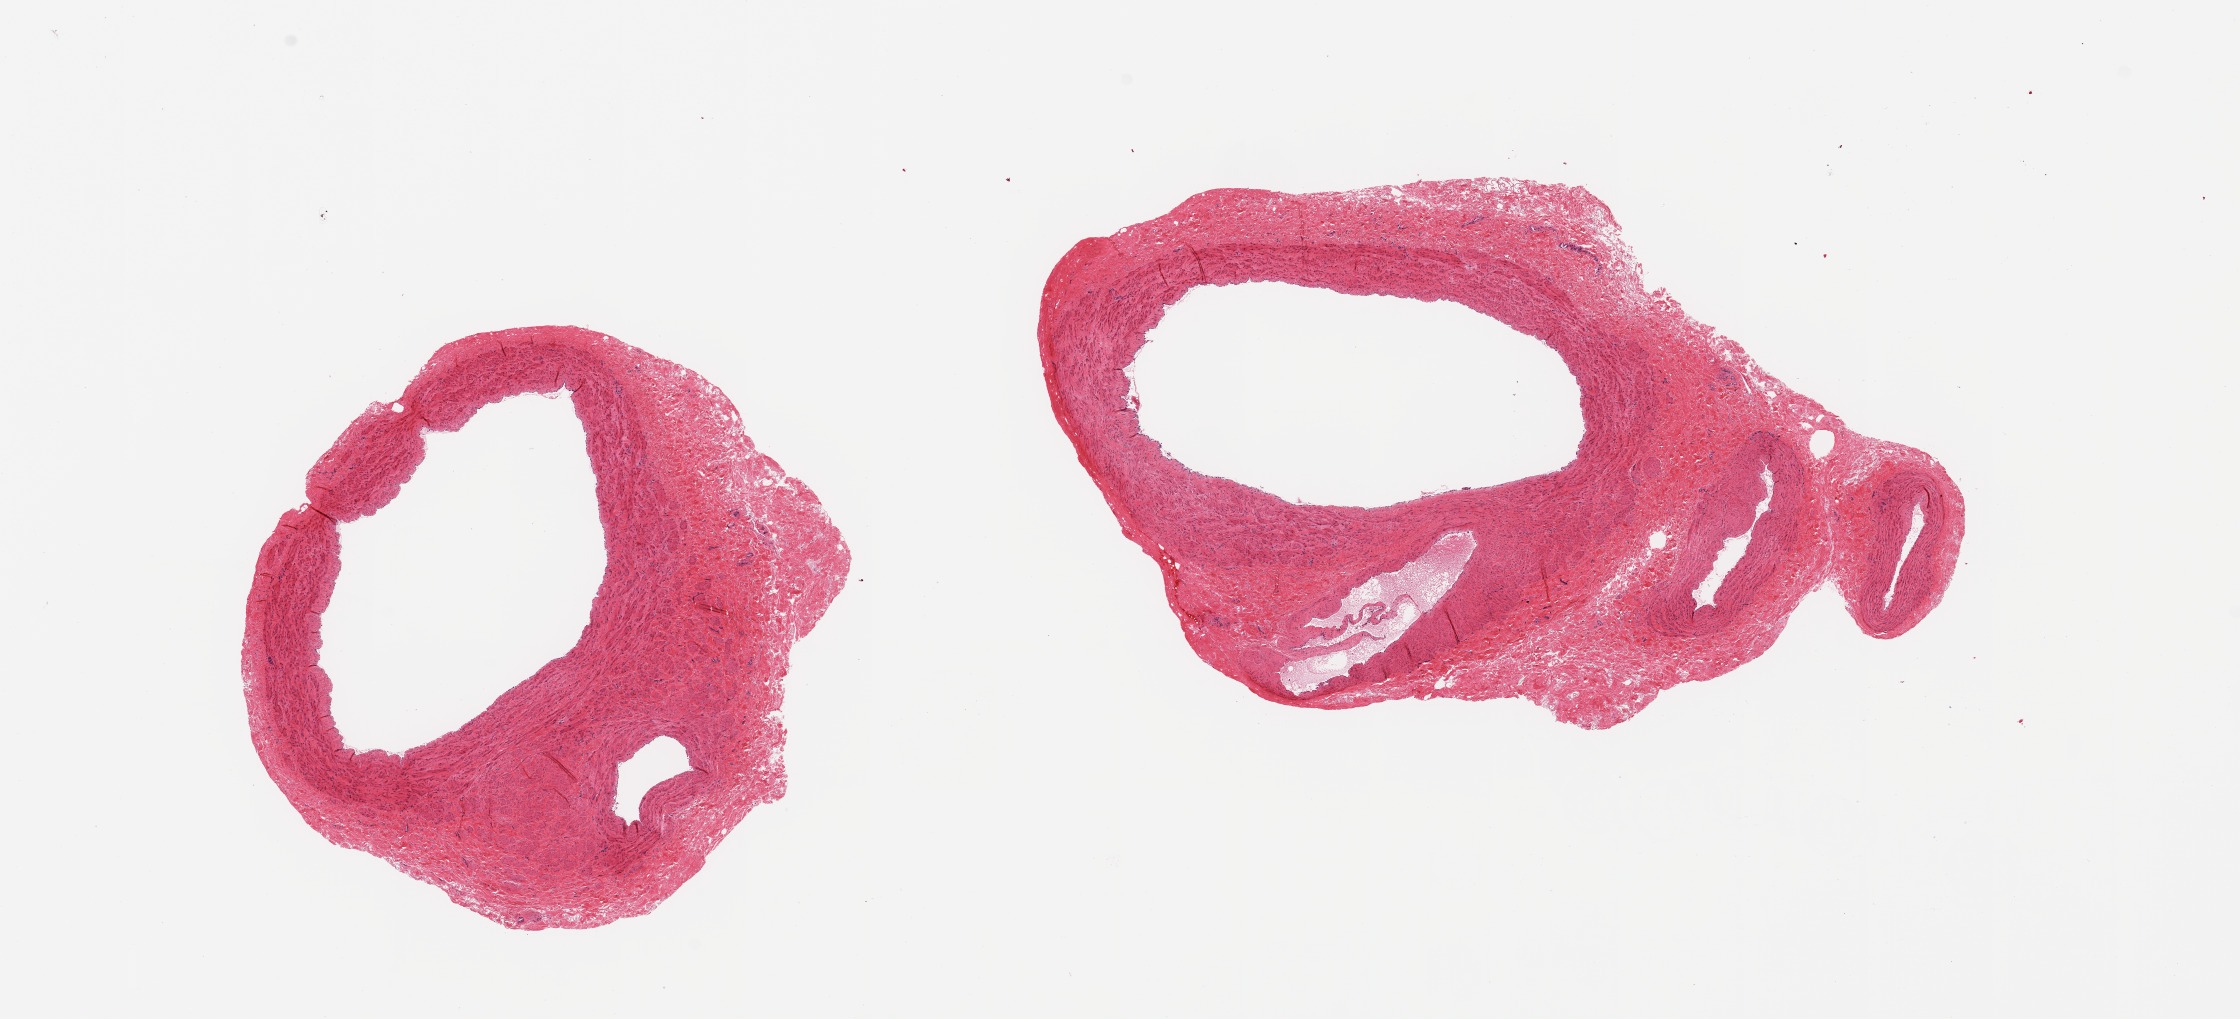
Hematoxylin and eosin (H&E) whole-slide image, brightfield, shown as a low-resolution overview of the whole scanned area (about 17.7 x 8.1 mm). PAXgene-fixed paraffin-embedded (PFPE) section. Sampled site (target tissue): tibial artery. Donor tissue sample.
Reviewer comment on this tissue sample: 2 pieces, no adherent fat; good specimen.